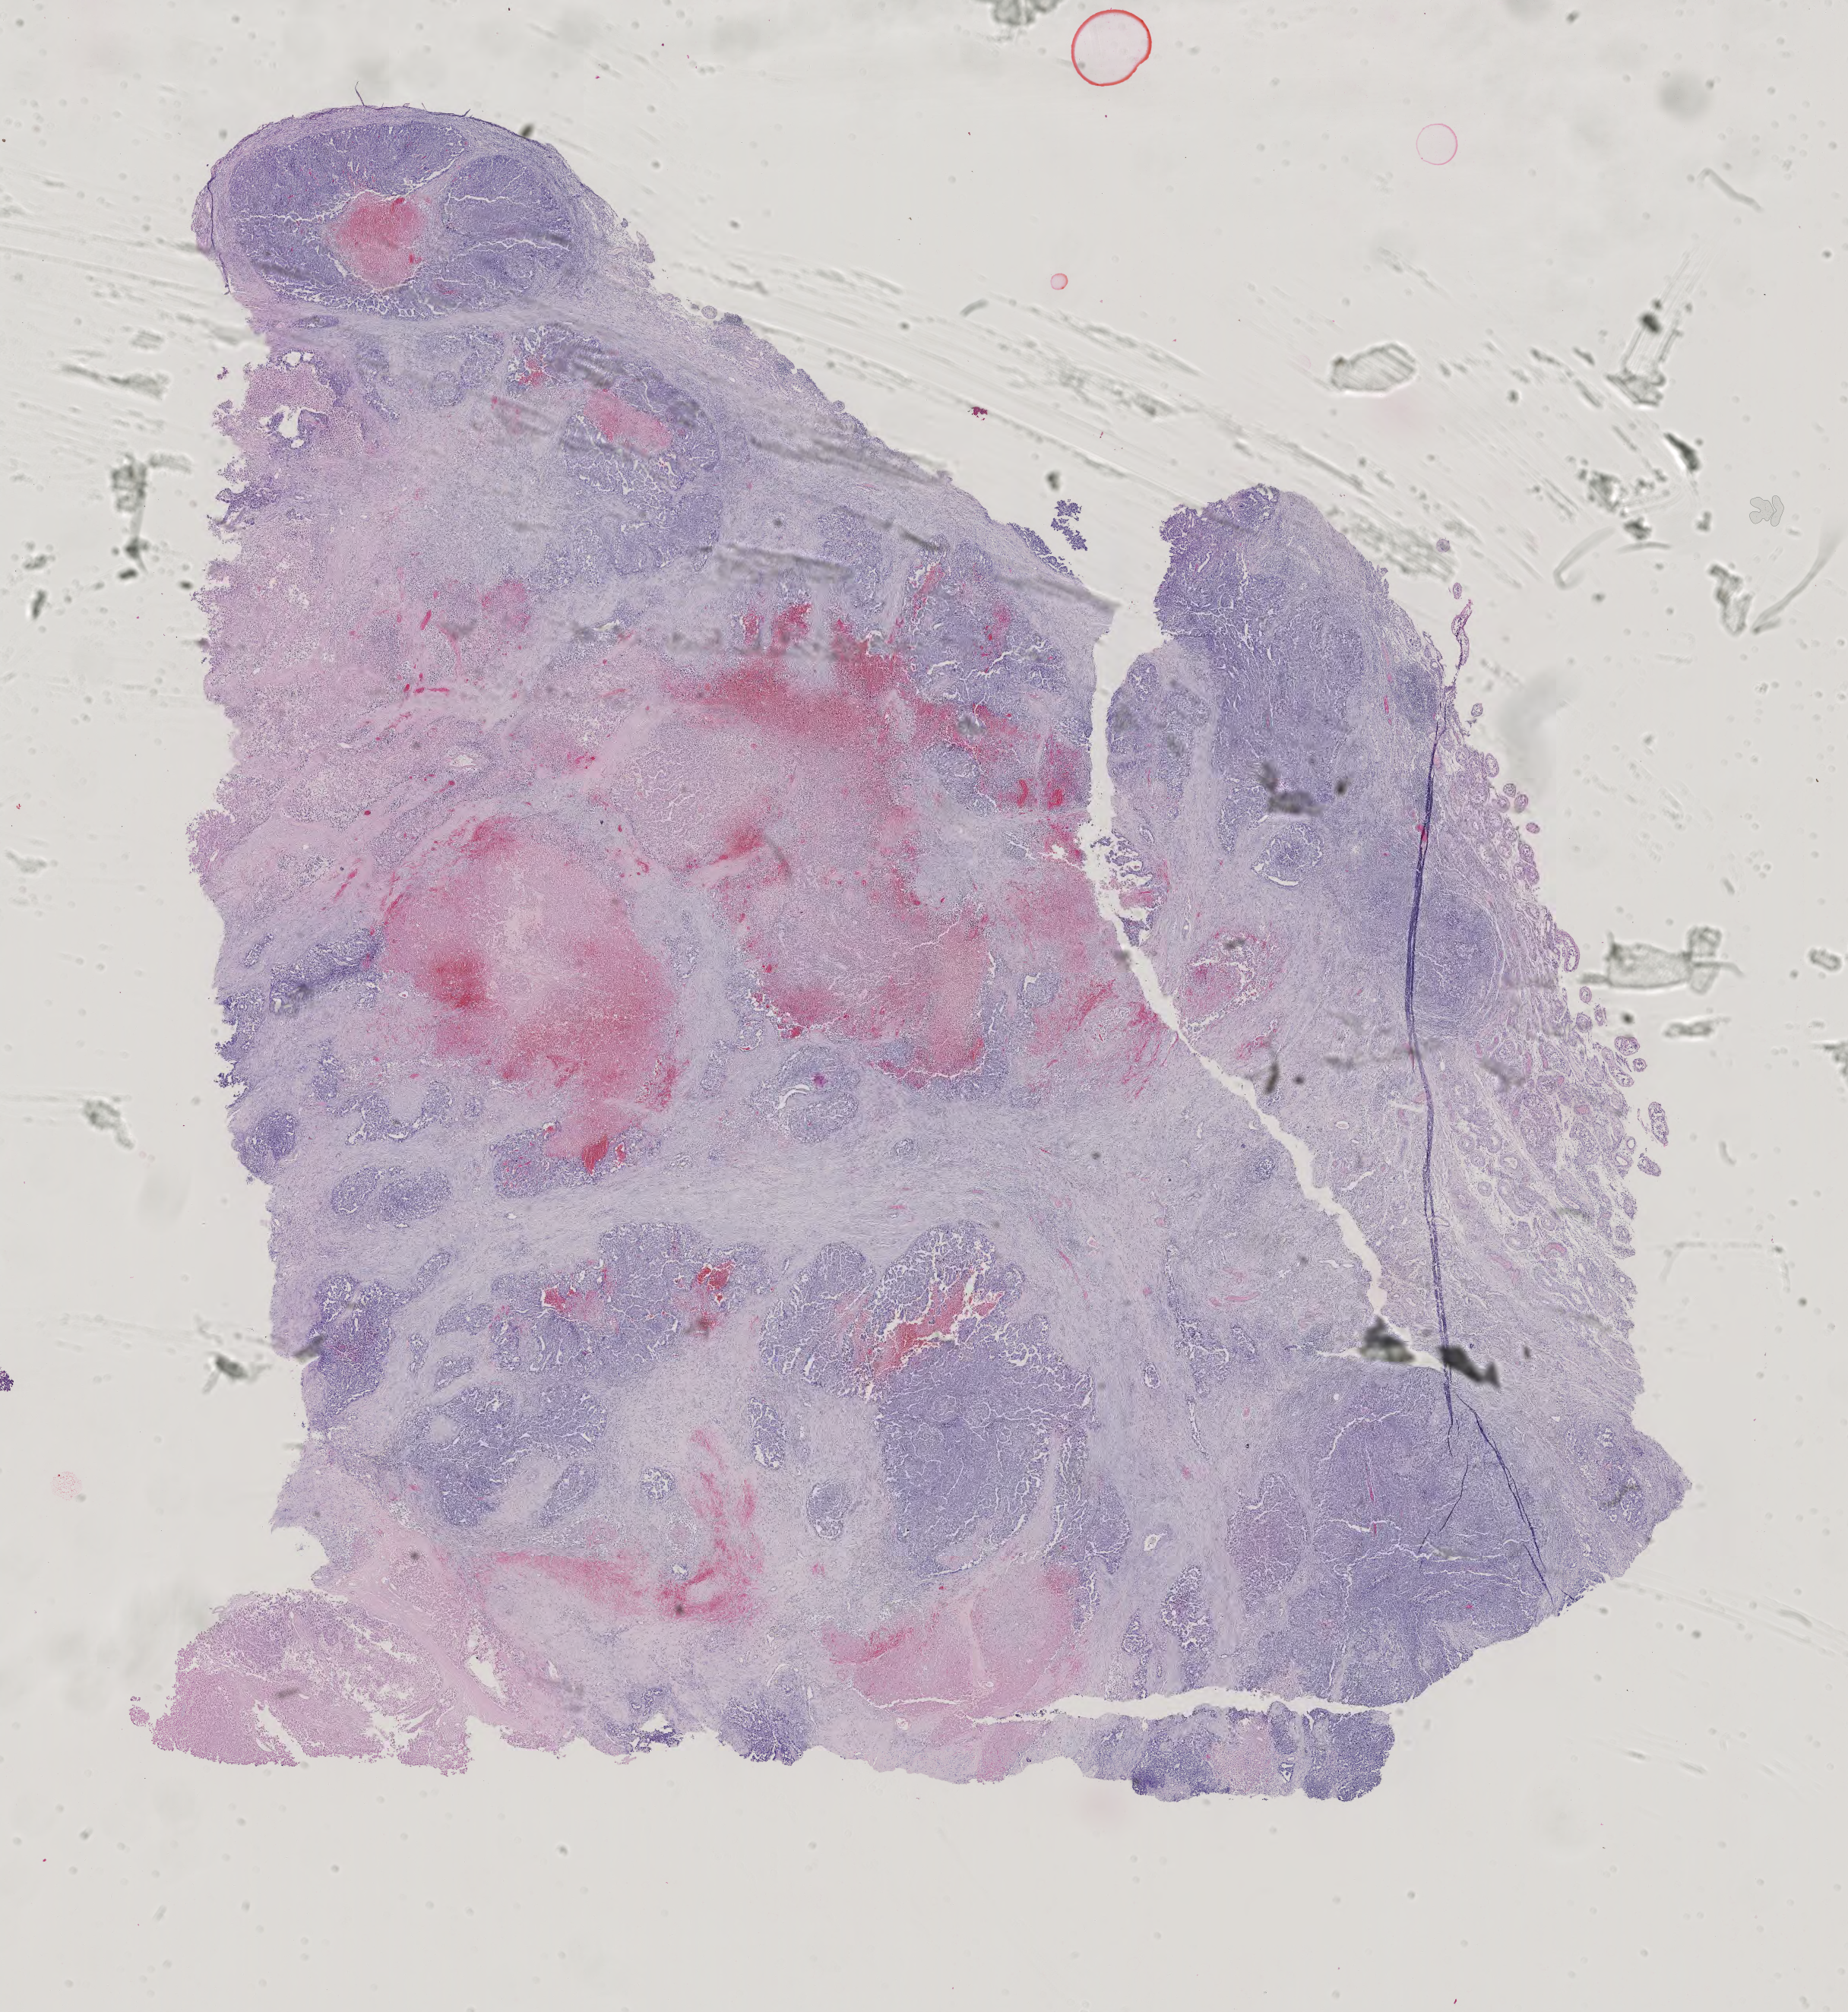
Whole-slide histology image, H&E — whole scanned area (about 17.7 x 19.3 mm, acquisition: 40x scan) shown as a low-resolution overview, formalin-fixed paraffin-embedded (FFPE) diagnostic section, testis, primary tumour sample. Male, age 24 years at initial diagnosis.
AJCC pathologic stage: IIA. Laterality: left. TNM: T2 N1 M0. Pathologic diagnosis: Embryonal carcinoma, NOS.